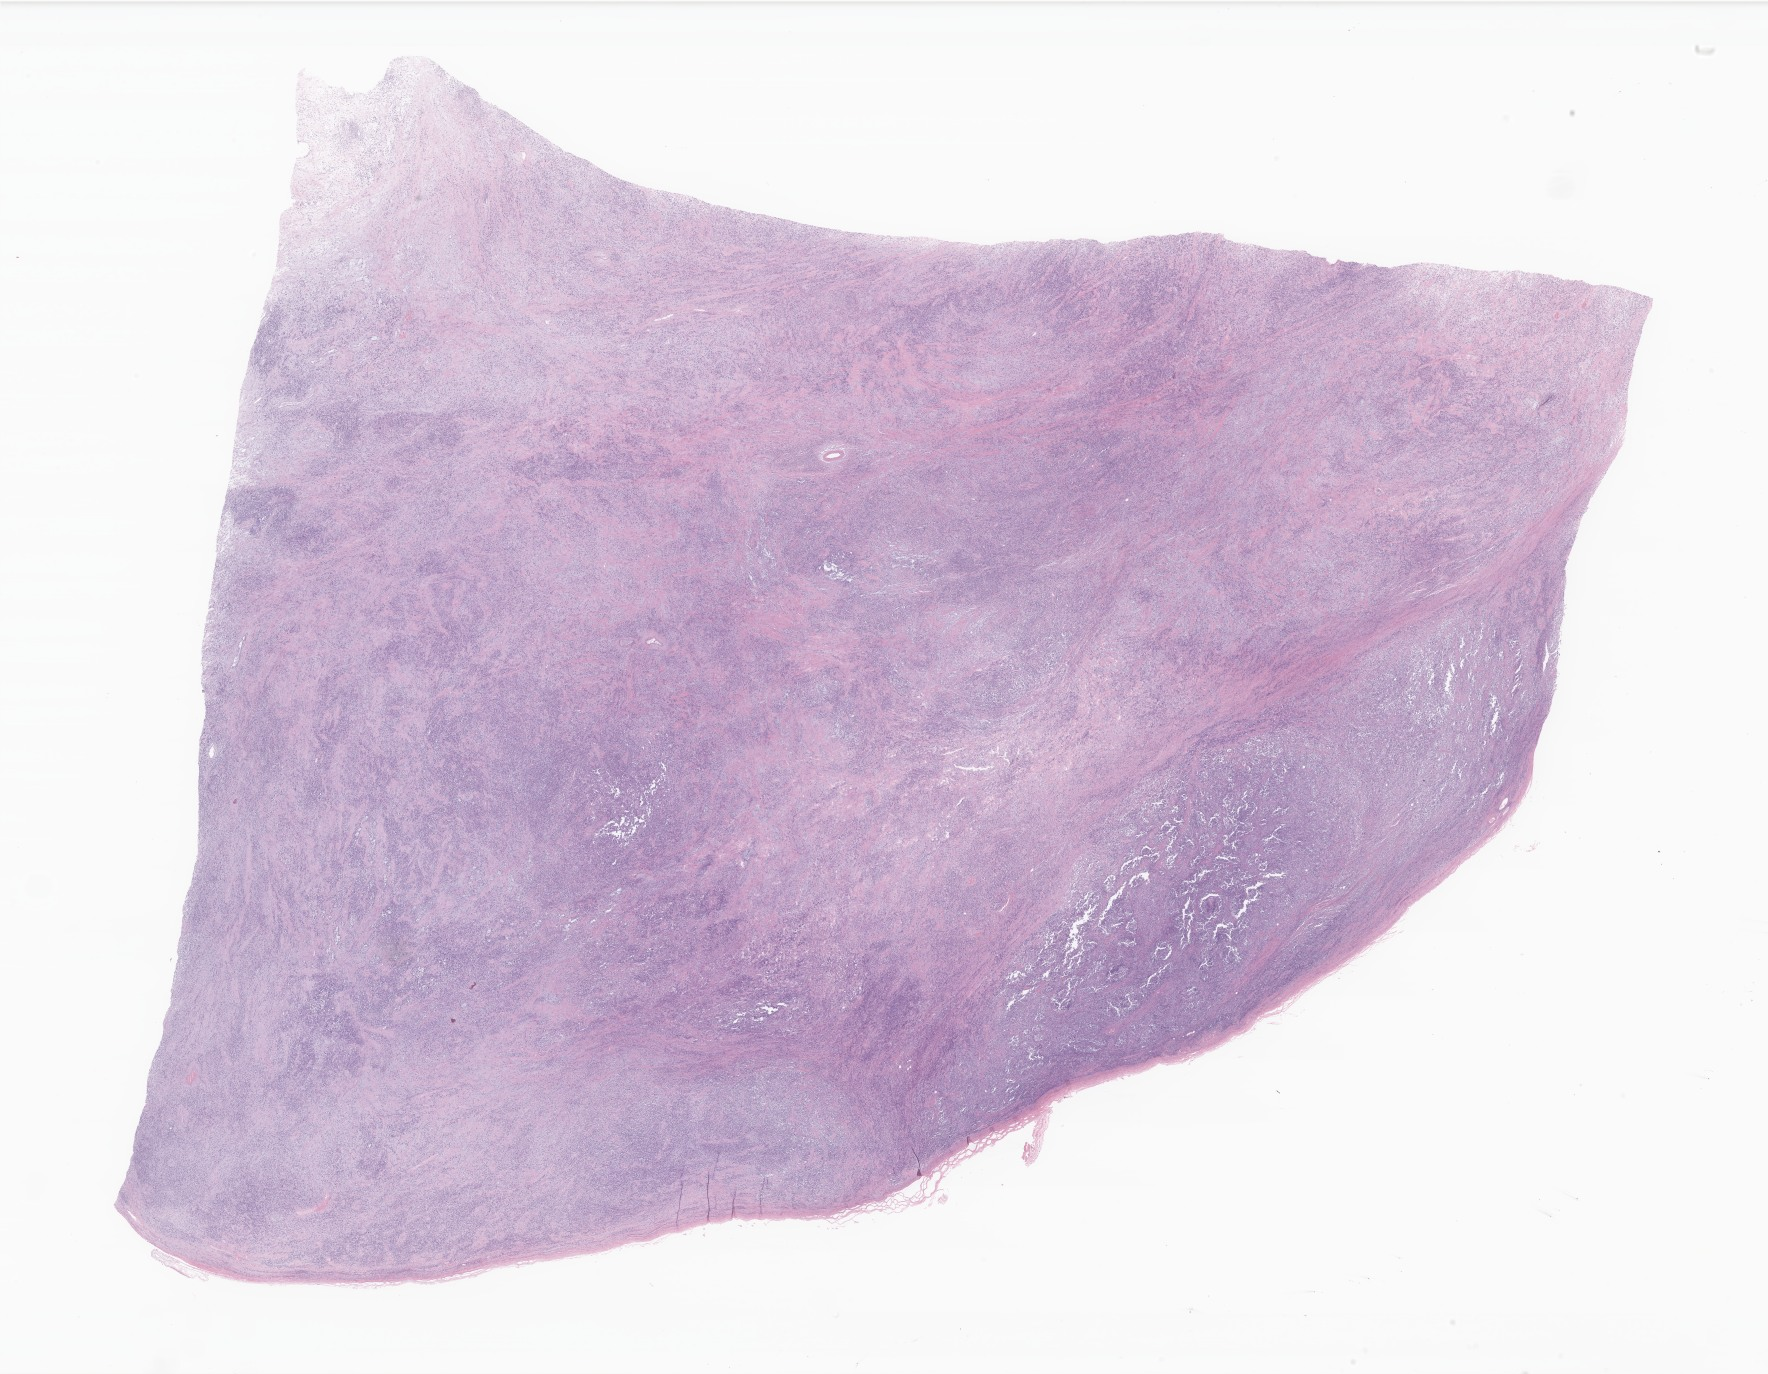
Whole-slide image, H&E stain of tumor tissue from the testis, low-resolution overview of the scanned area, about 29.8 x 23.2 mm, formalin-fixed, paraffin-embedded (FFPE) tissue. Male patient, age 222 months (18 years 6 months).
Diagnosis: Embryonal rhabdomyosarcoma, NOS.